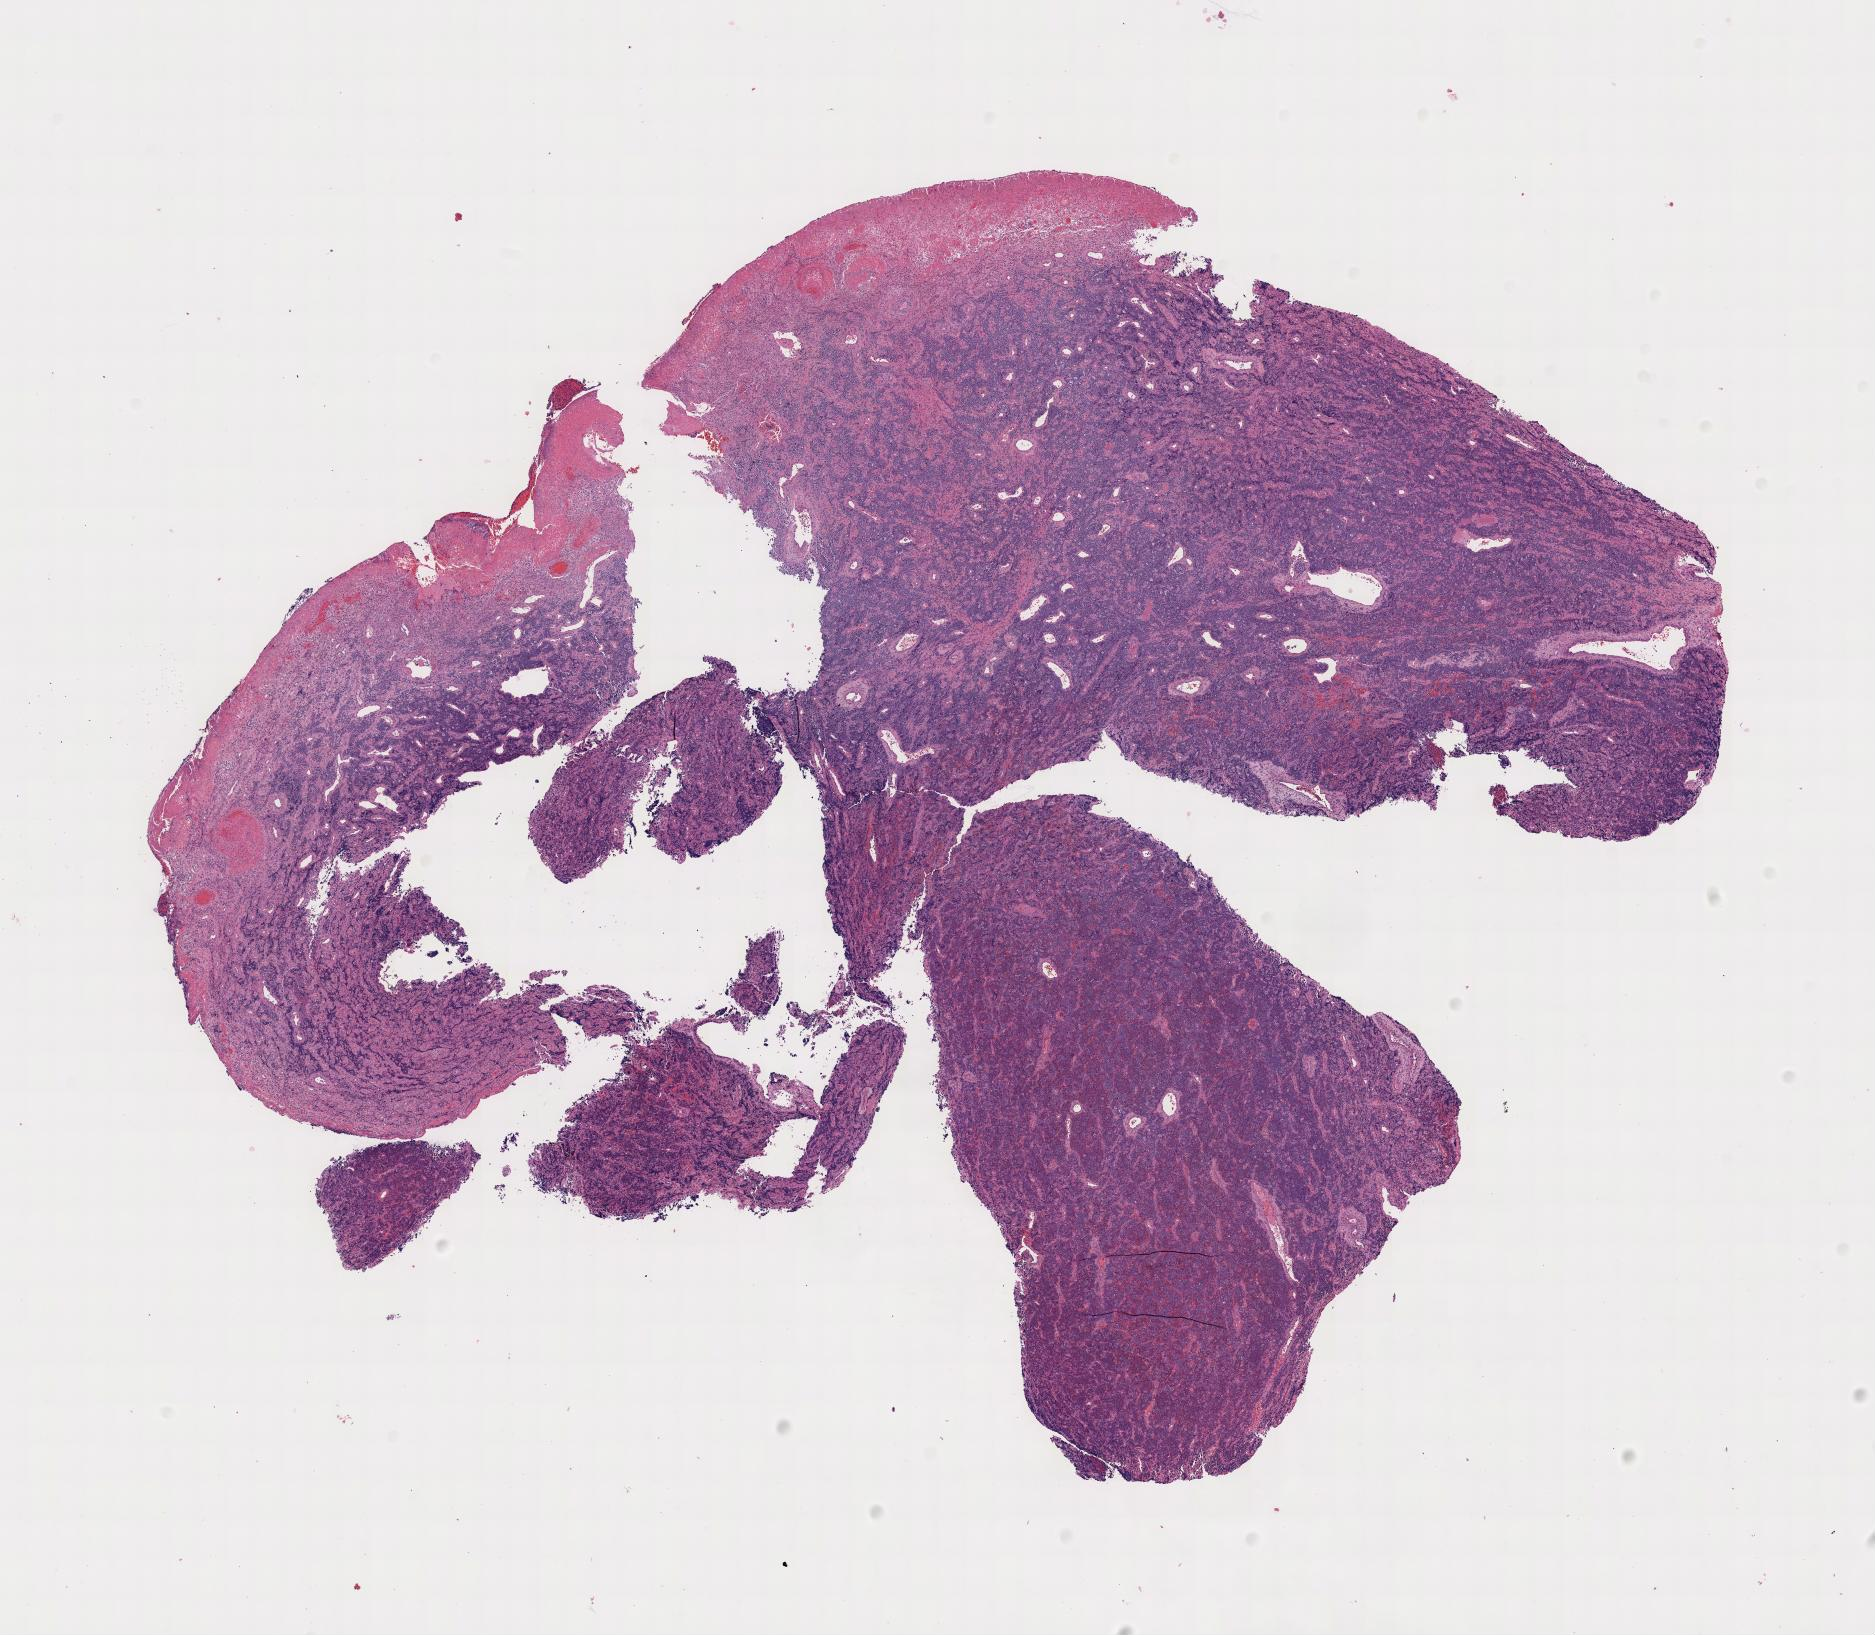
Haematoxylin and eosin whole-slide image — a low-resolution overview of the entire scanned area, specimen: tumor tissue, site: cranium. Patient: male, age at initial diagnosis 7 years.
- histologic diagnosis: Burkitt lymphoma, NOS